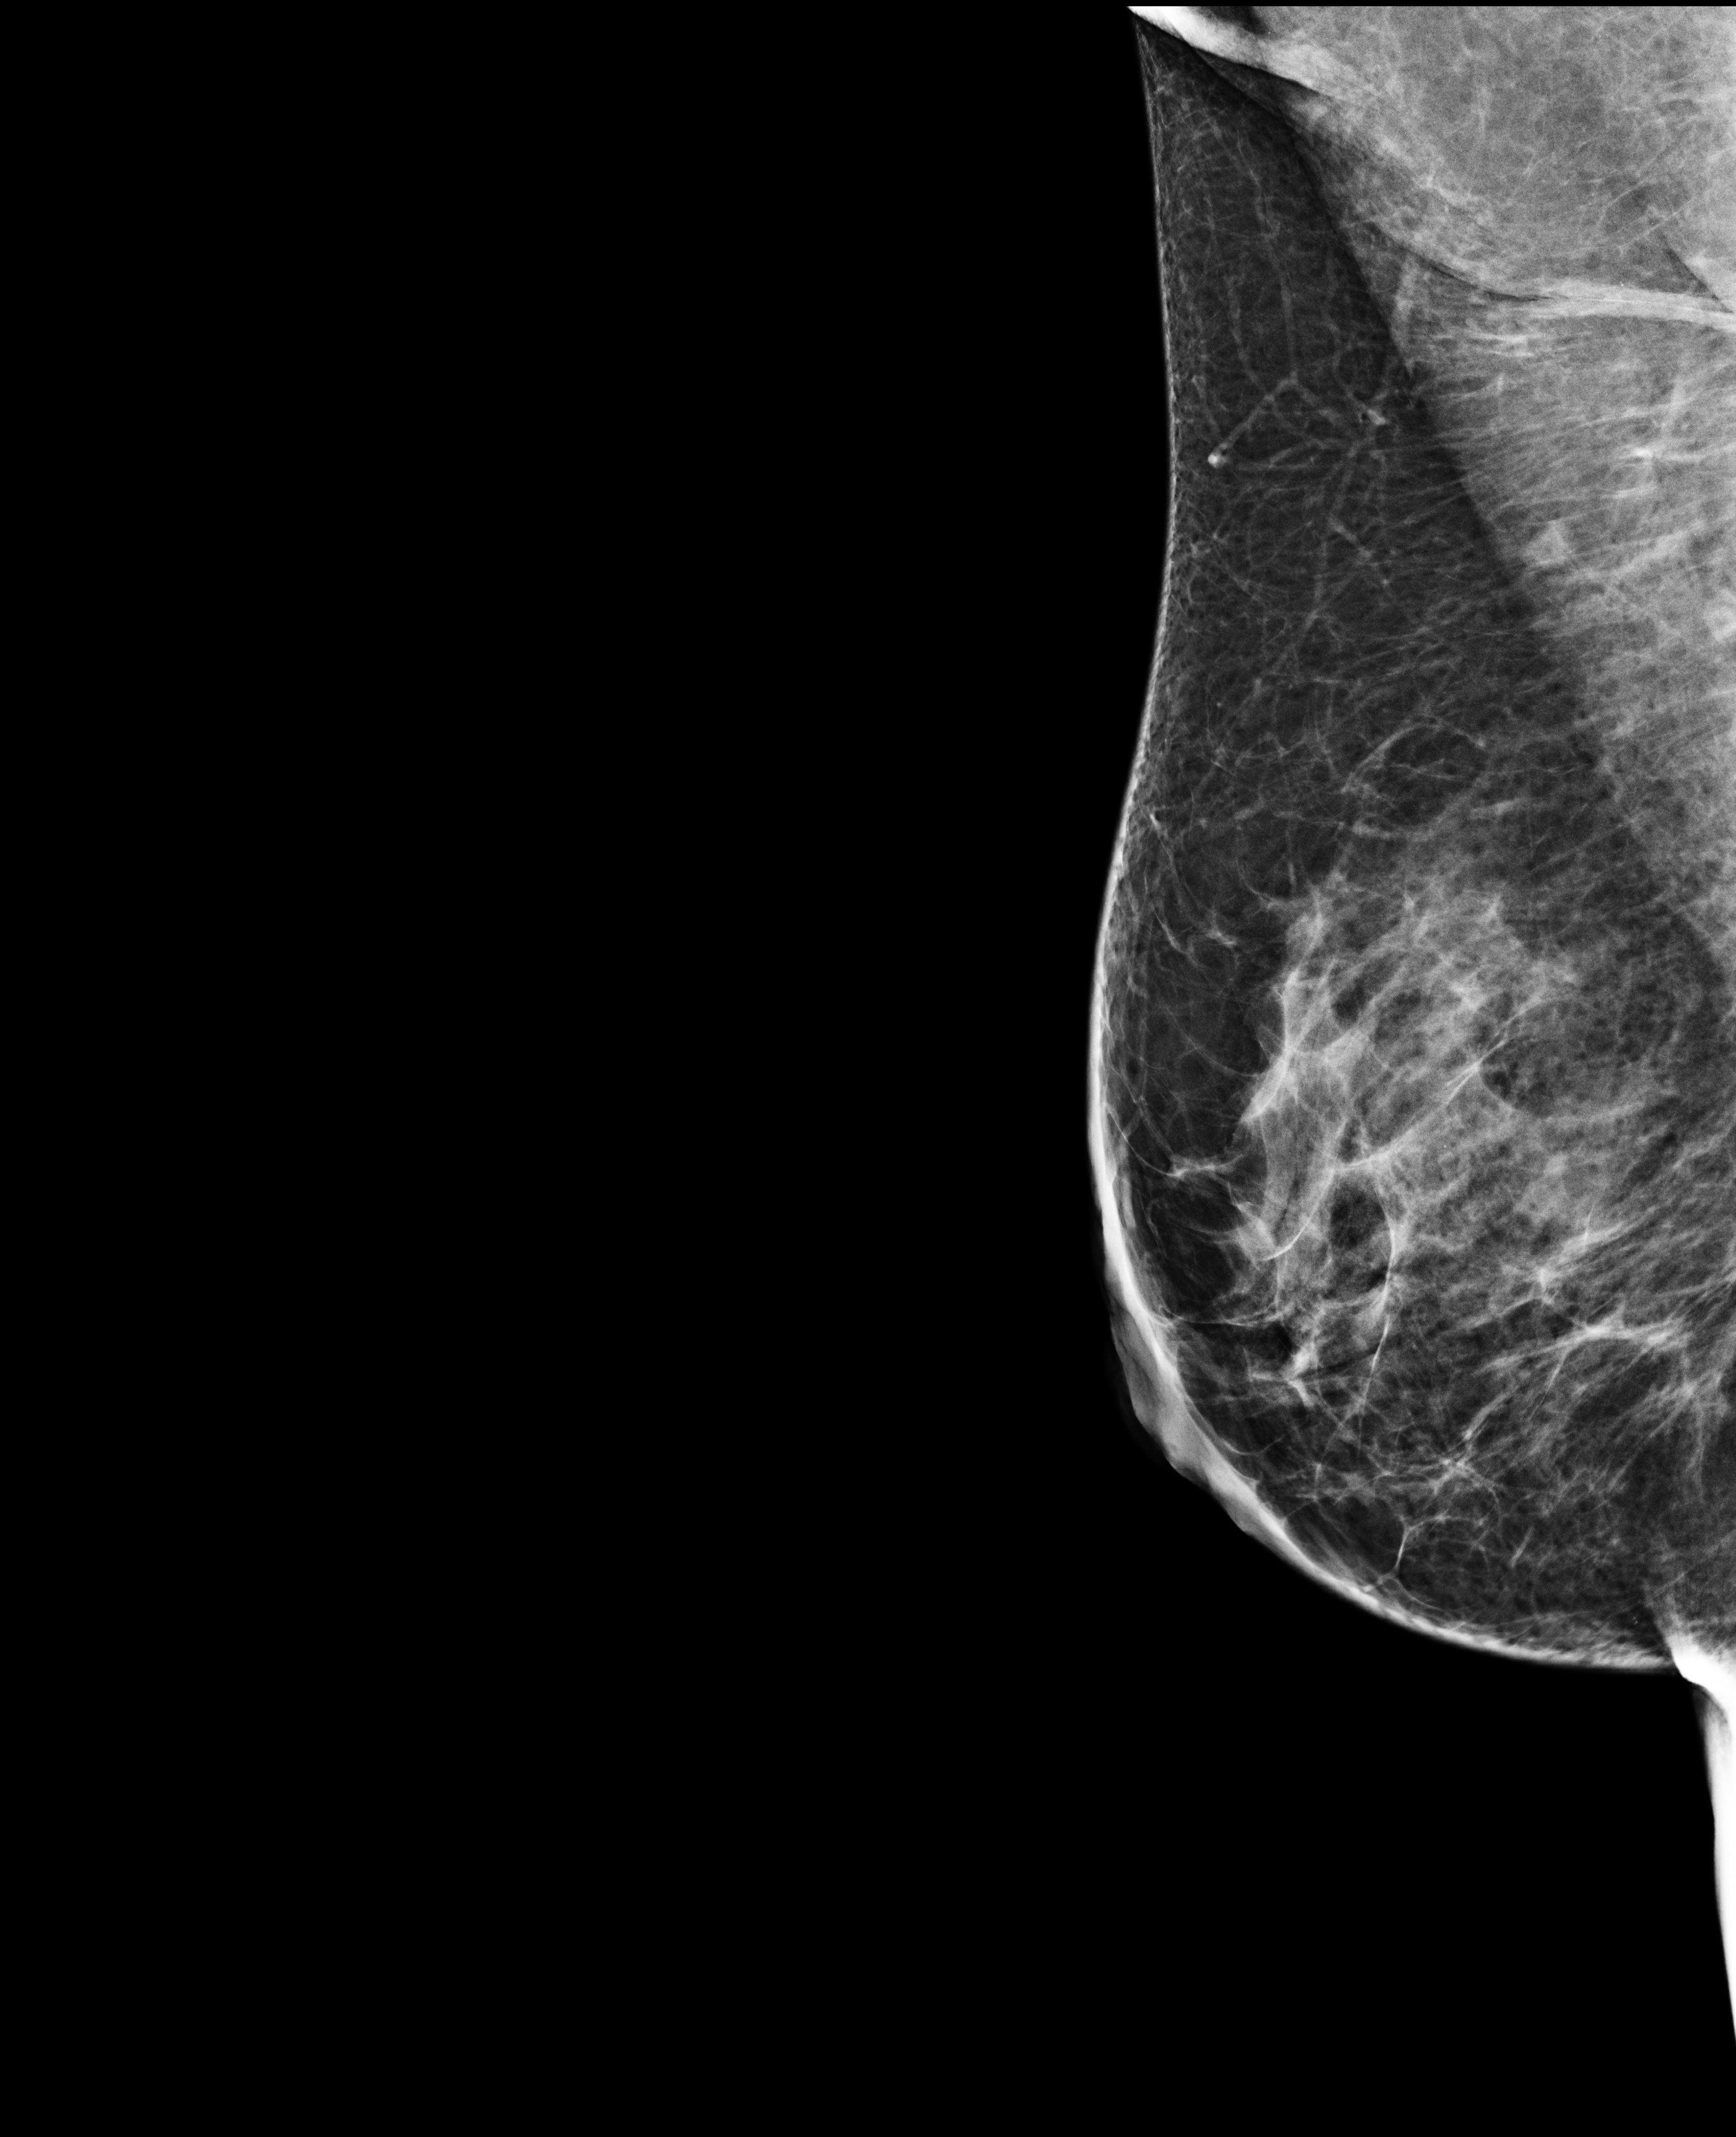
Annual screening mammography examination, compressed breast thickness 56 mm, system: Selenia Dimensions. Patient aged 47 years (female).
Image type: full-field digital mammogram. Breast: right. Projection: mediolateral oblique (MLO) view.